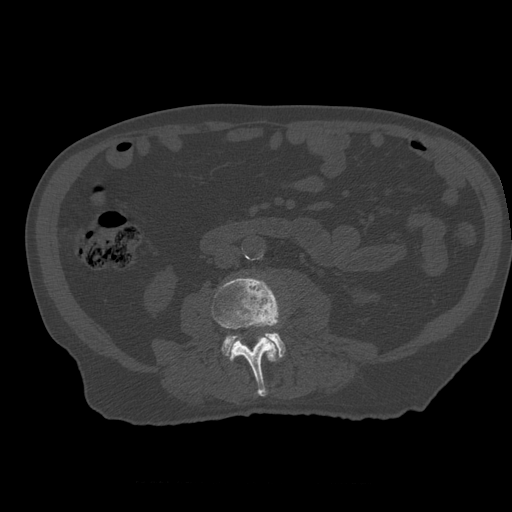
CT including the spine, one axial slice. Position 182 of 399 along the scan axis. Reconstruction kernel STANDARD. 120 kVp. Bone window (W 1800 / L 400 HU). 1.25 mm slice thickness. 512 × 512 image matrix. Patient age 73 years. Case-level facts recorded for this patient, not image findings: primary cancer: prostate; vertebrae with lytic lesions (as recorded): L2.
Outlined on this slice (semi-automatically segmented with operator editing):
- L3 vertebra: bounding box <212,277,281,397> (left, top, right, bottom; pixels)
- L4 vertebra: <222,333,286,358>